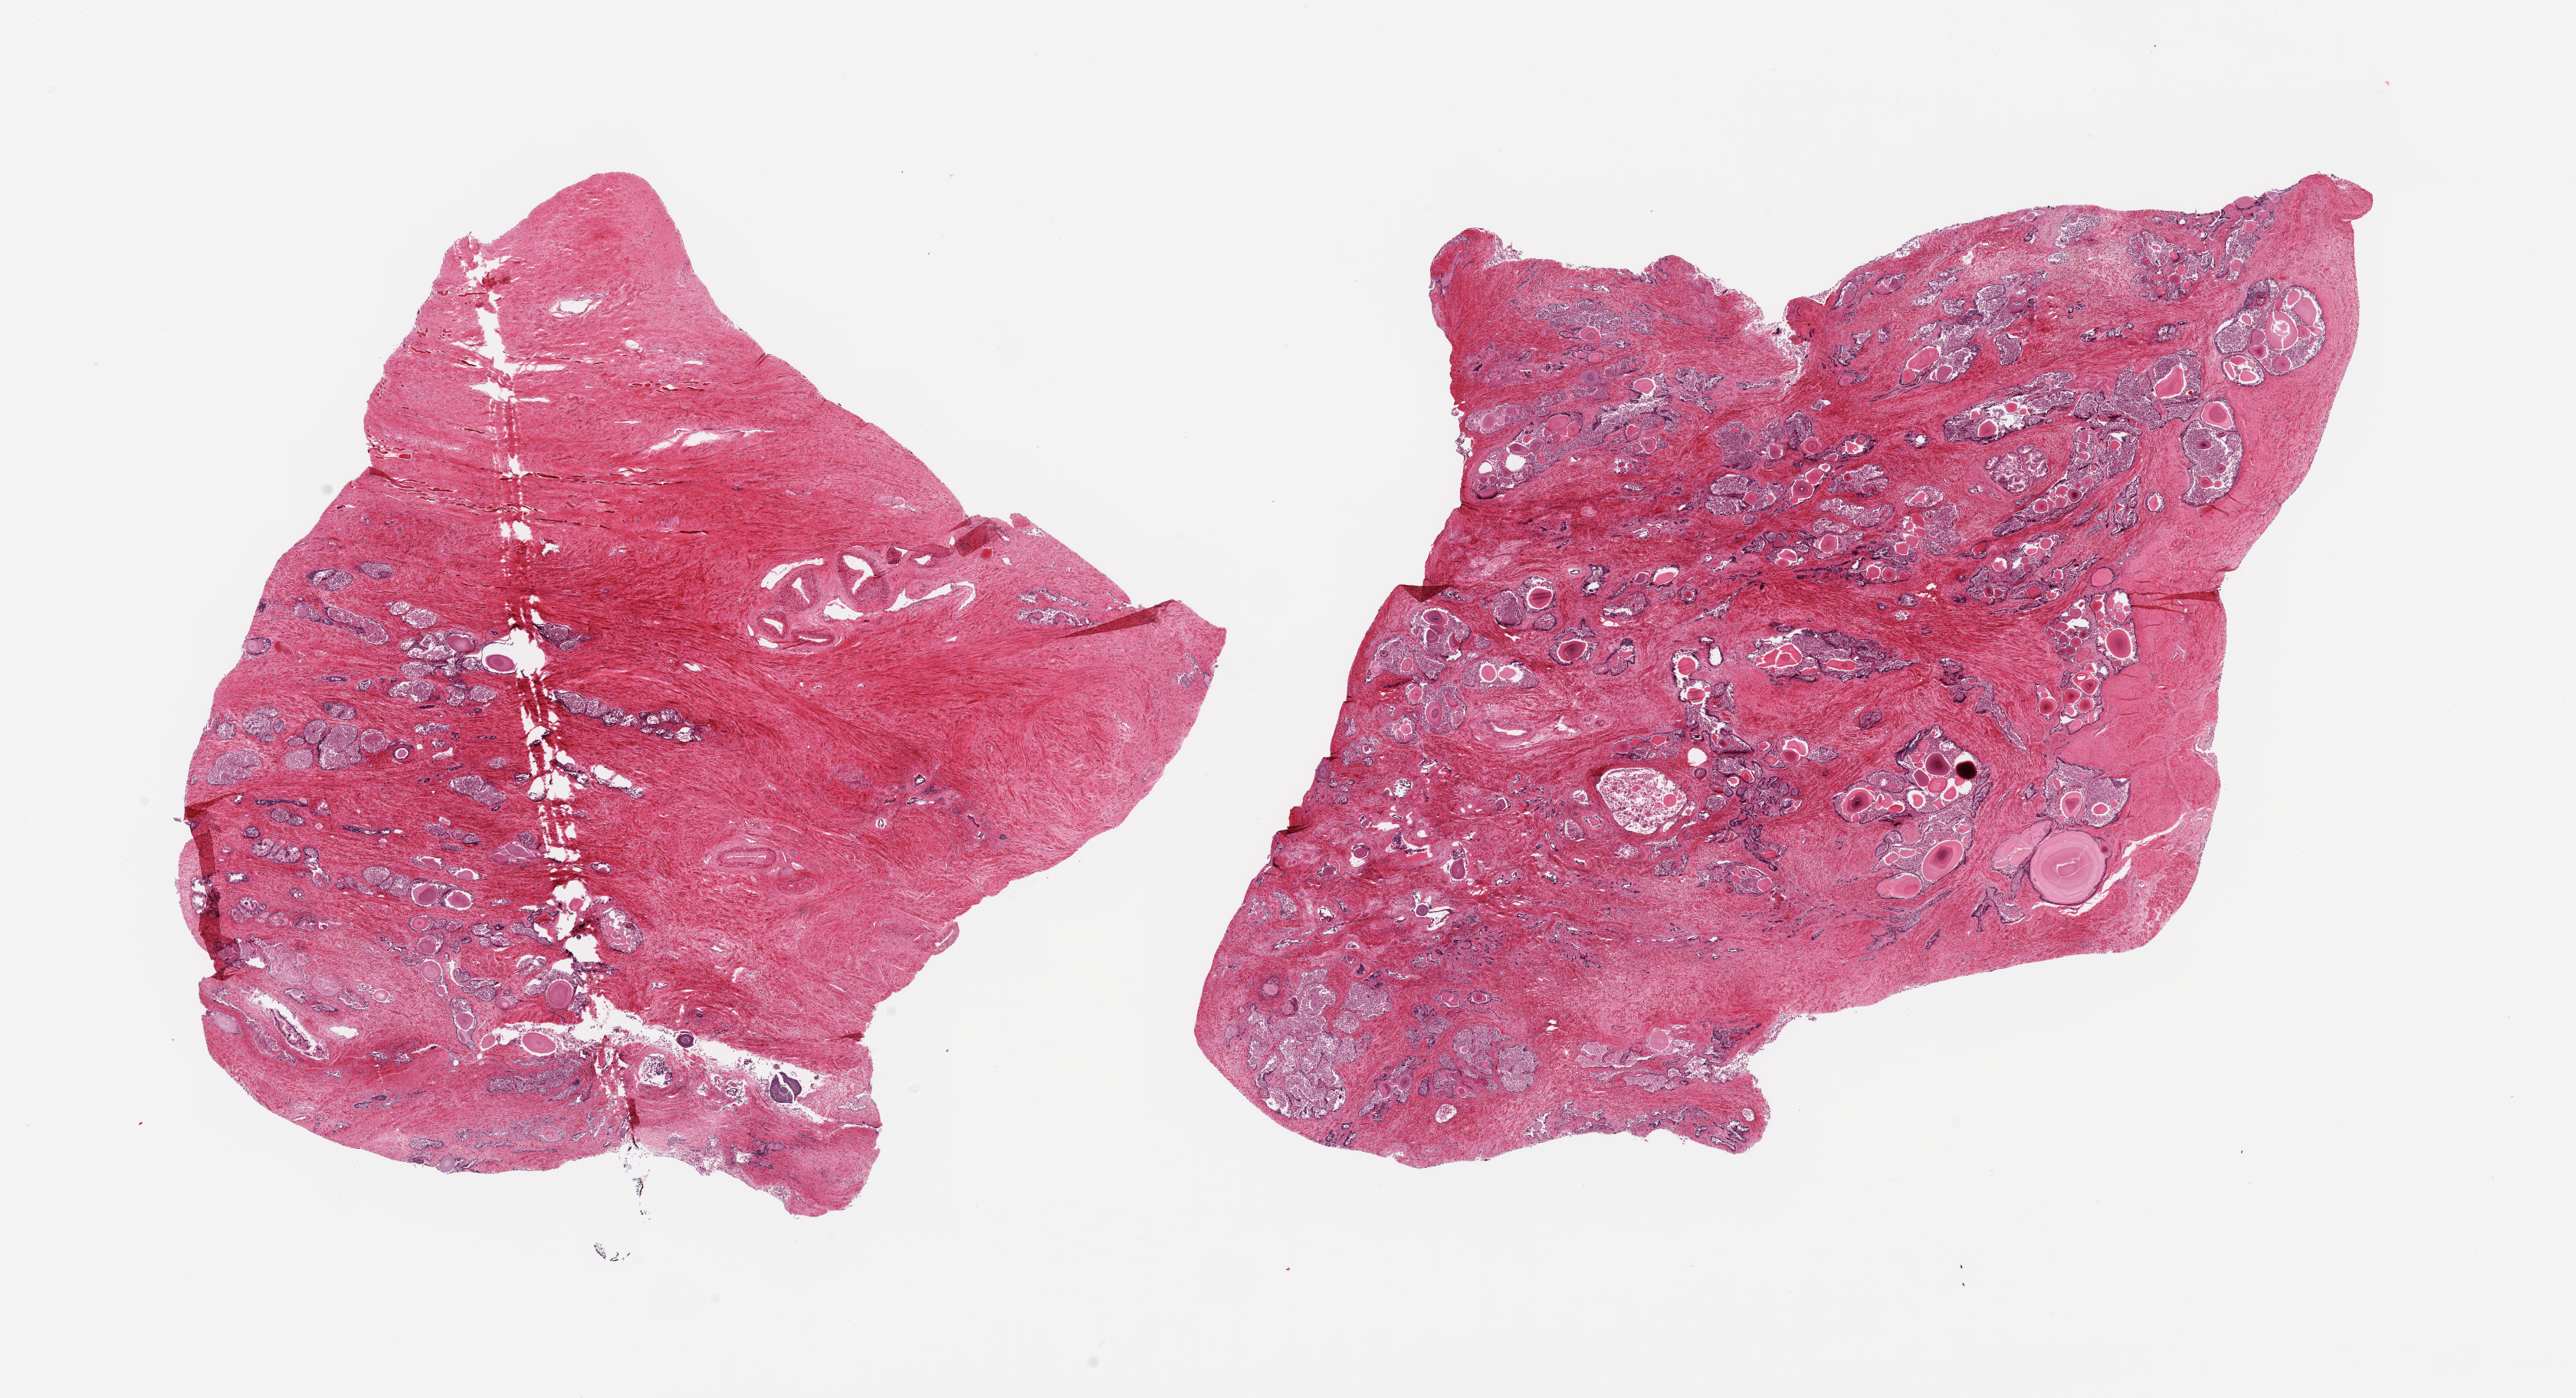
H&E whole-slide image — whole scanned area (about 26.6 x 14.4 mm) shown as a low-resolution overview; PAXgene-fixed paraffin-embedded (PFPE) section; target tissue: prostate; donor tissue sample. Donor sex: male.
Review note (as recorded): 2 pieces, glandular component with advanced autolysis, hyperplastic glandular and stromal pattern.